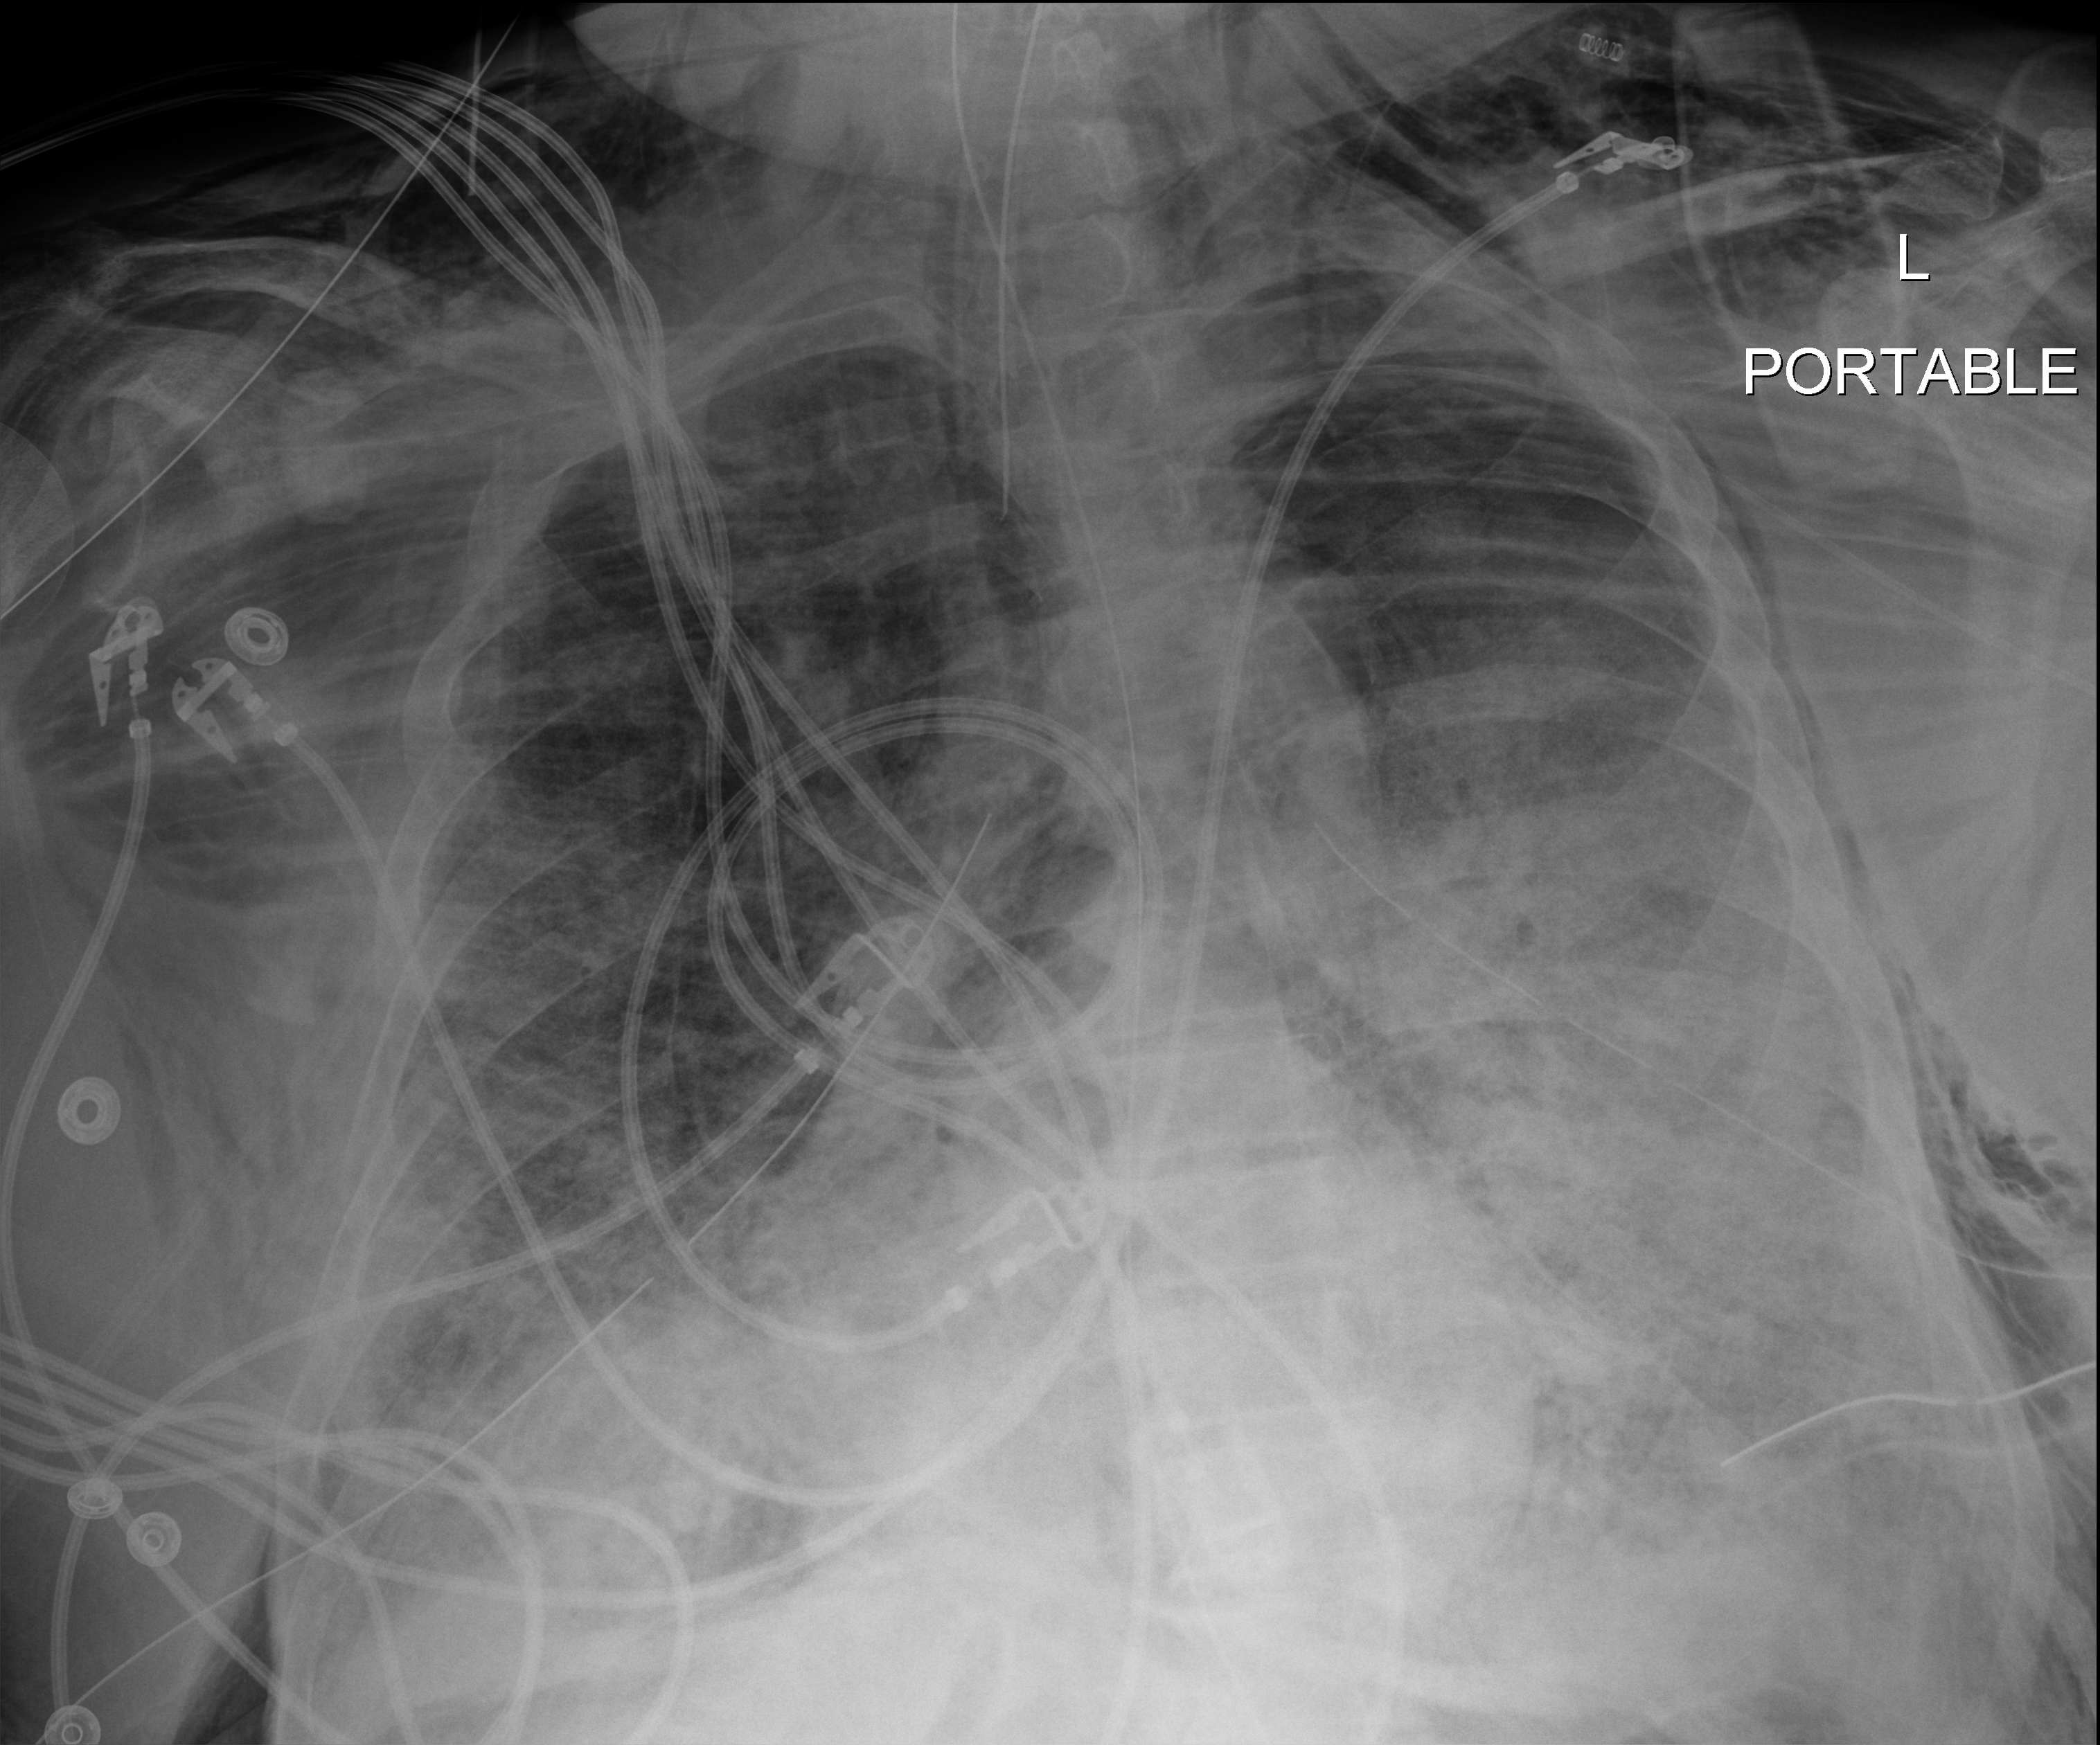
Chest X-ray (portable), anteroposterior (AP) projection. Adult patient hospitalised with COVID-19, age 18–59 years.
Hospital-stay facts (about this admission, not read from this image; timing relative to this image not recorded):
- admitted to intensive care during this hospital stay: yes
- mechanically ventilated during this hospital stay: yes